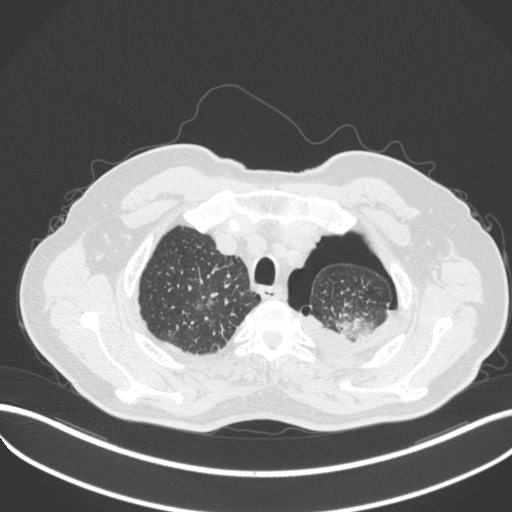
Chest CT, one axial slice; position 425 of 466 along the scan axis; reconstruction kernel B31f; 120 kVp; lung window (W 1500 / L -600 HU); 512 × 512 image matrix, field of view 400 × 400 mm. Patient: male, 76 years. From the clinical record (not read from this slice): clinical TNM (as recorded): T3 N0 M1b.
Outlined on this slice (bounding box drawn by a radiologist):
- lung tumour (recorded histology: adenocarcinoma): box from (x=331, y=300) to (x=373, y=340) px